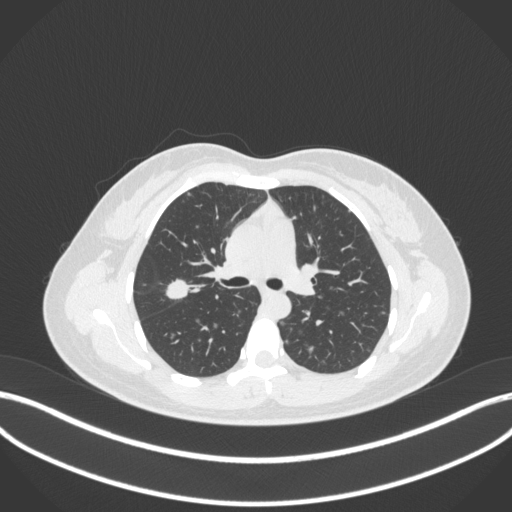
Chest CT, one axial slice; position 211 of 214 along the scan axis; reconstruction kernel B31f; lung window (W 1500 / L -600 HU); 1 mm slice thickness; 512 × 512 image matrix, field of view 400 × 400 mm. Patient: female, 33 years. Case-level facts recorded for this patient, not image findings: clinical TNM (as recorded): T1c N0 M0.
Annotated regions visible in this slice (rectangle marked by the reading radiologist):
- lung tumour (recorded histology: adenocarcinoma): box from (x=165, y=277) to (x=191, y=303) px